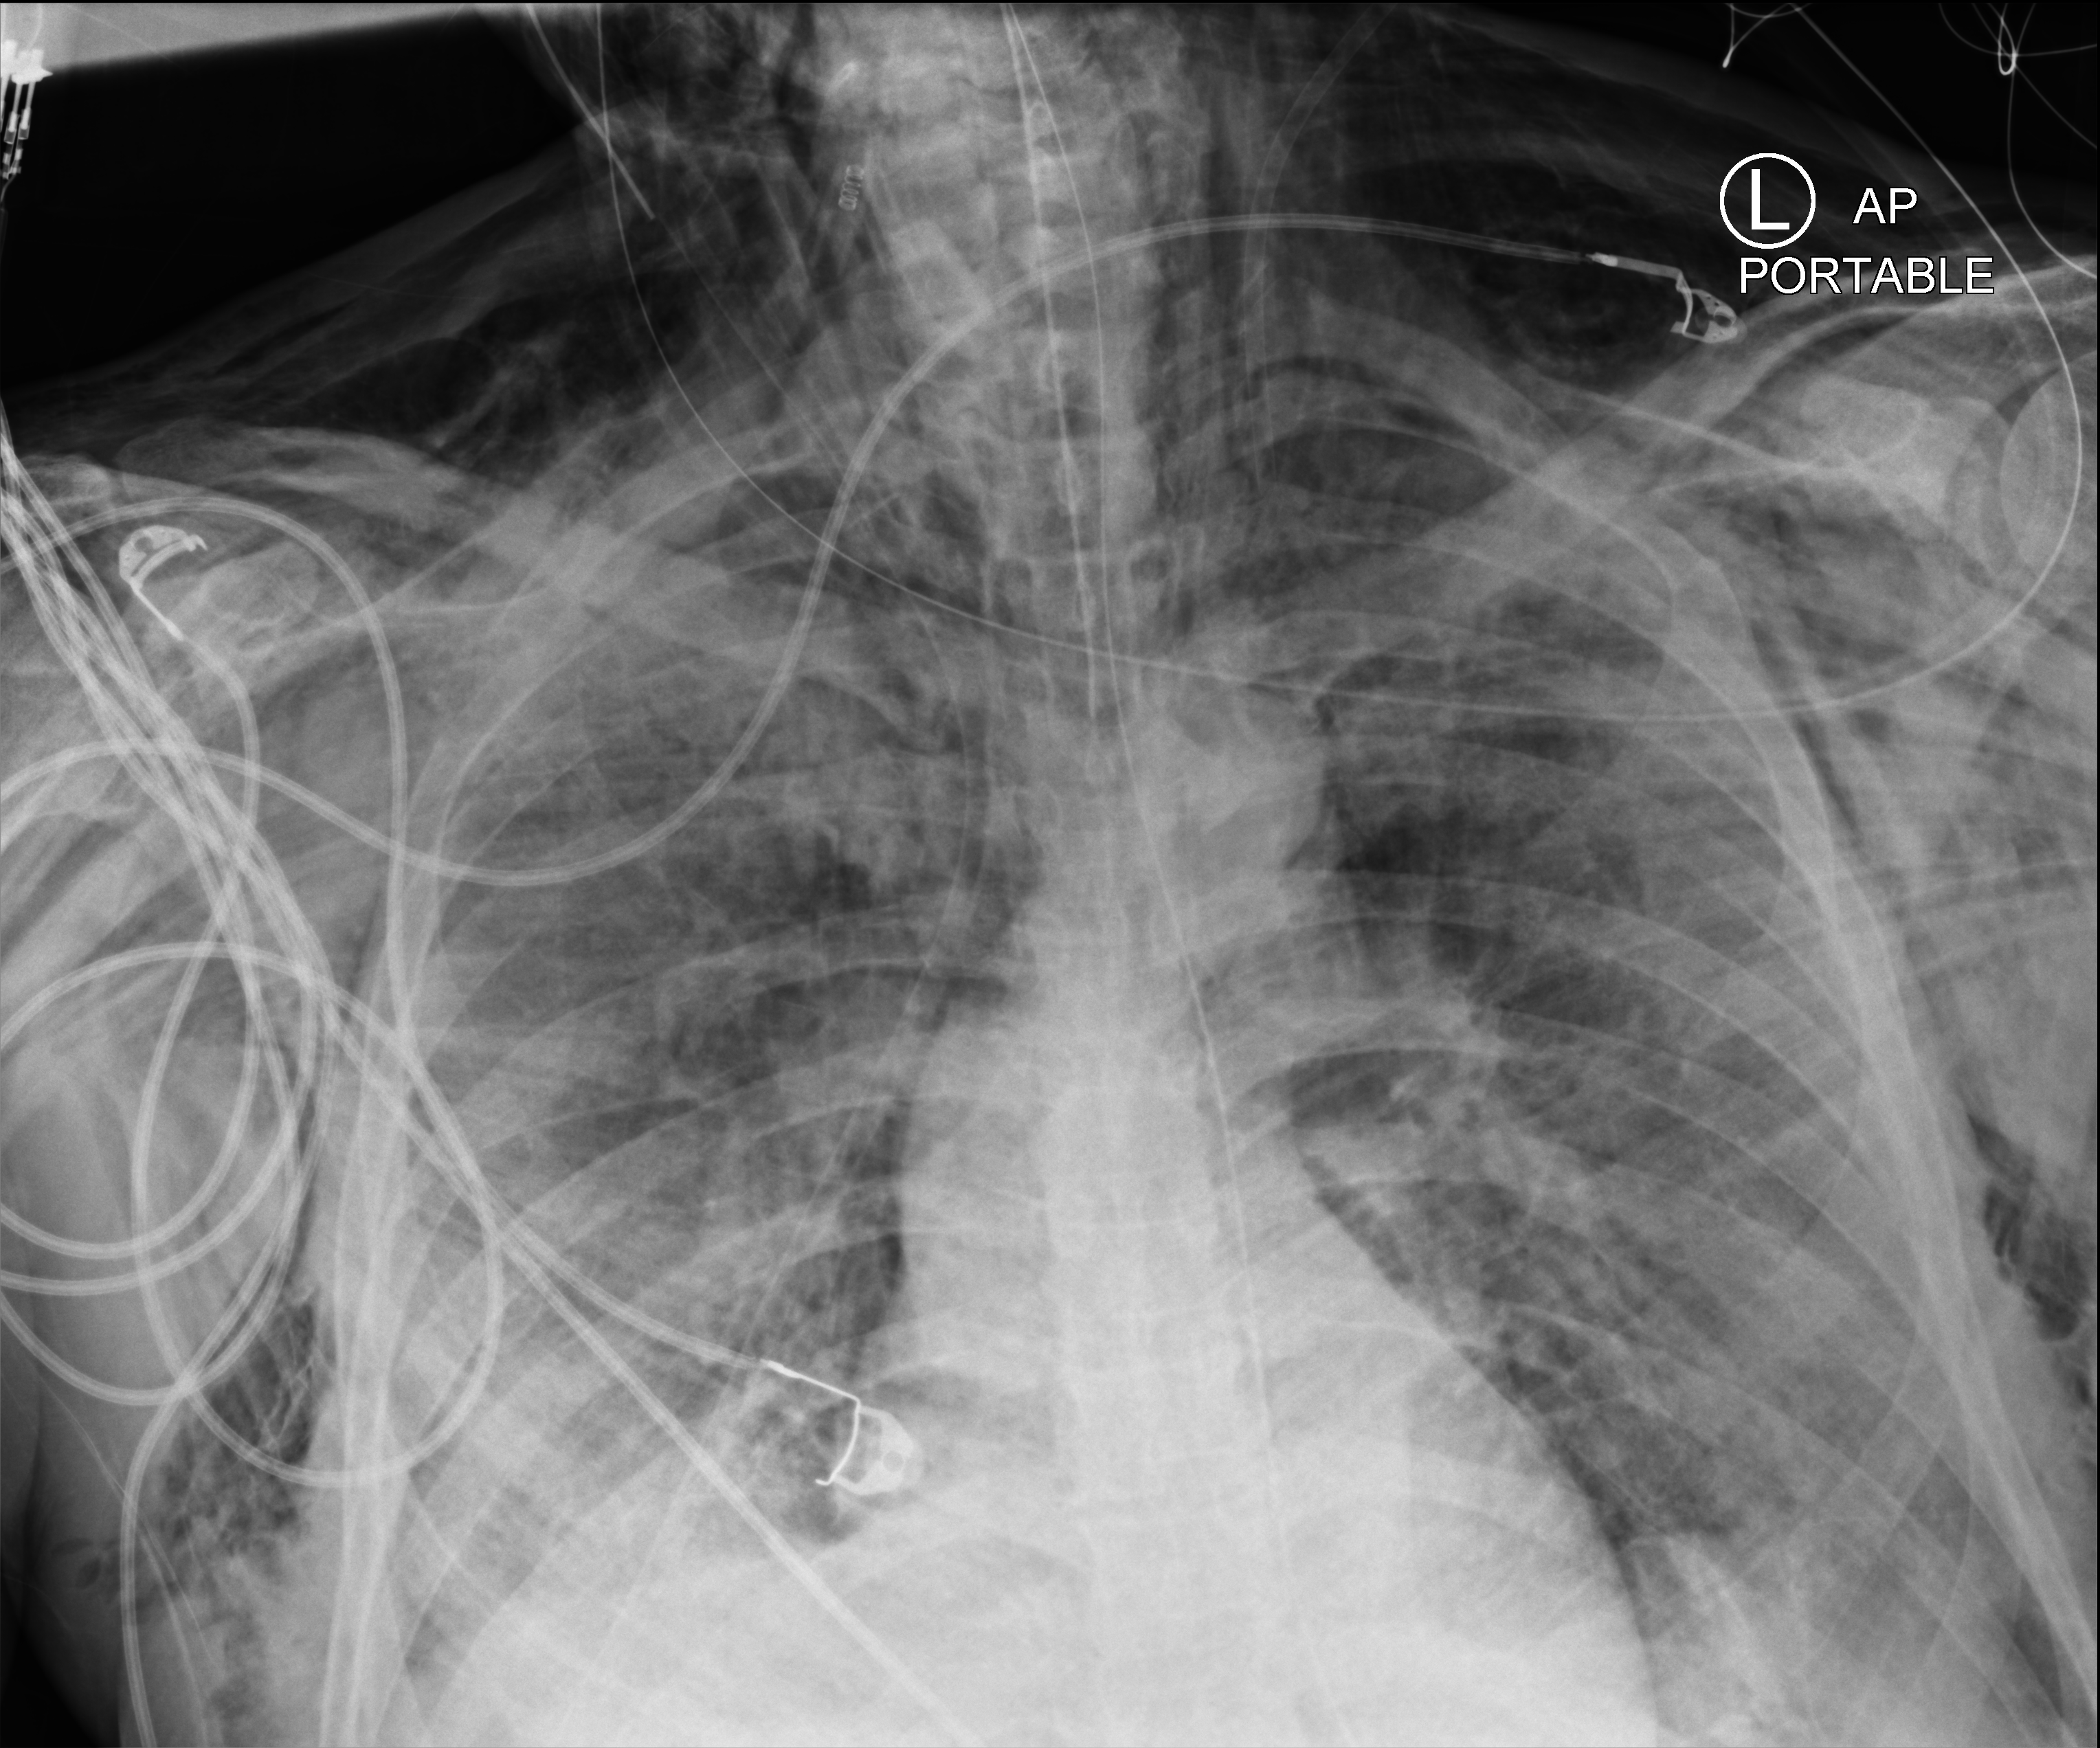
Portable chest radiograph, anteroposterior (AP) projection. Male patient hospitalised with COVID-19, age 60–74 years.
Admission-level facts for this patient (not findings on this image; timing relative to this image not recorded):
- COPD (admission record): no